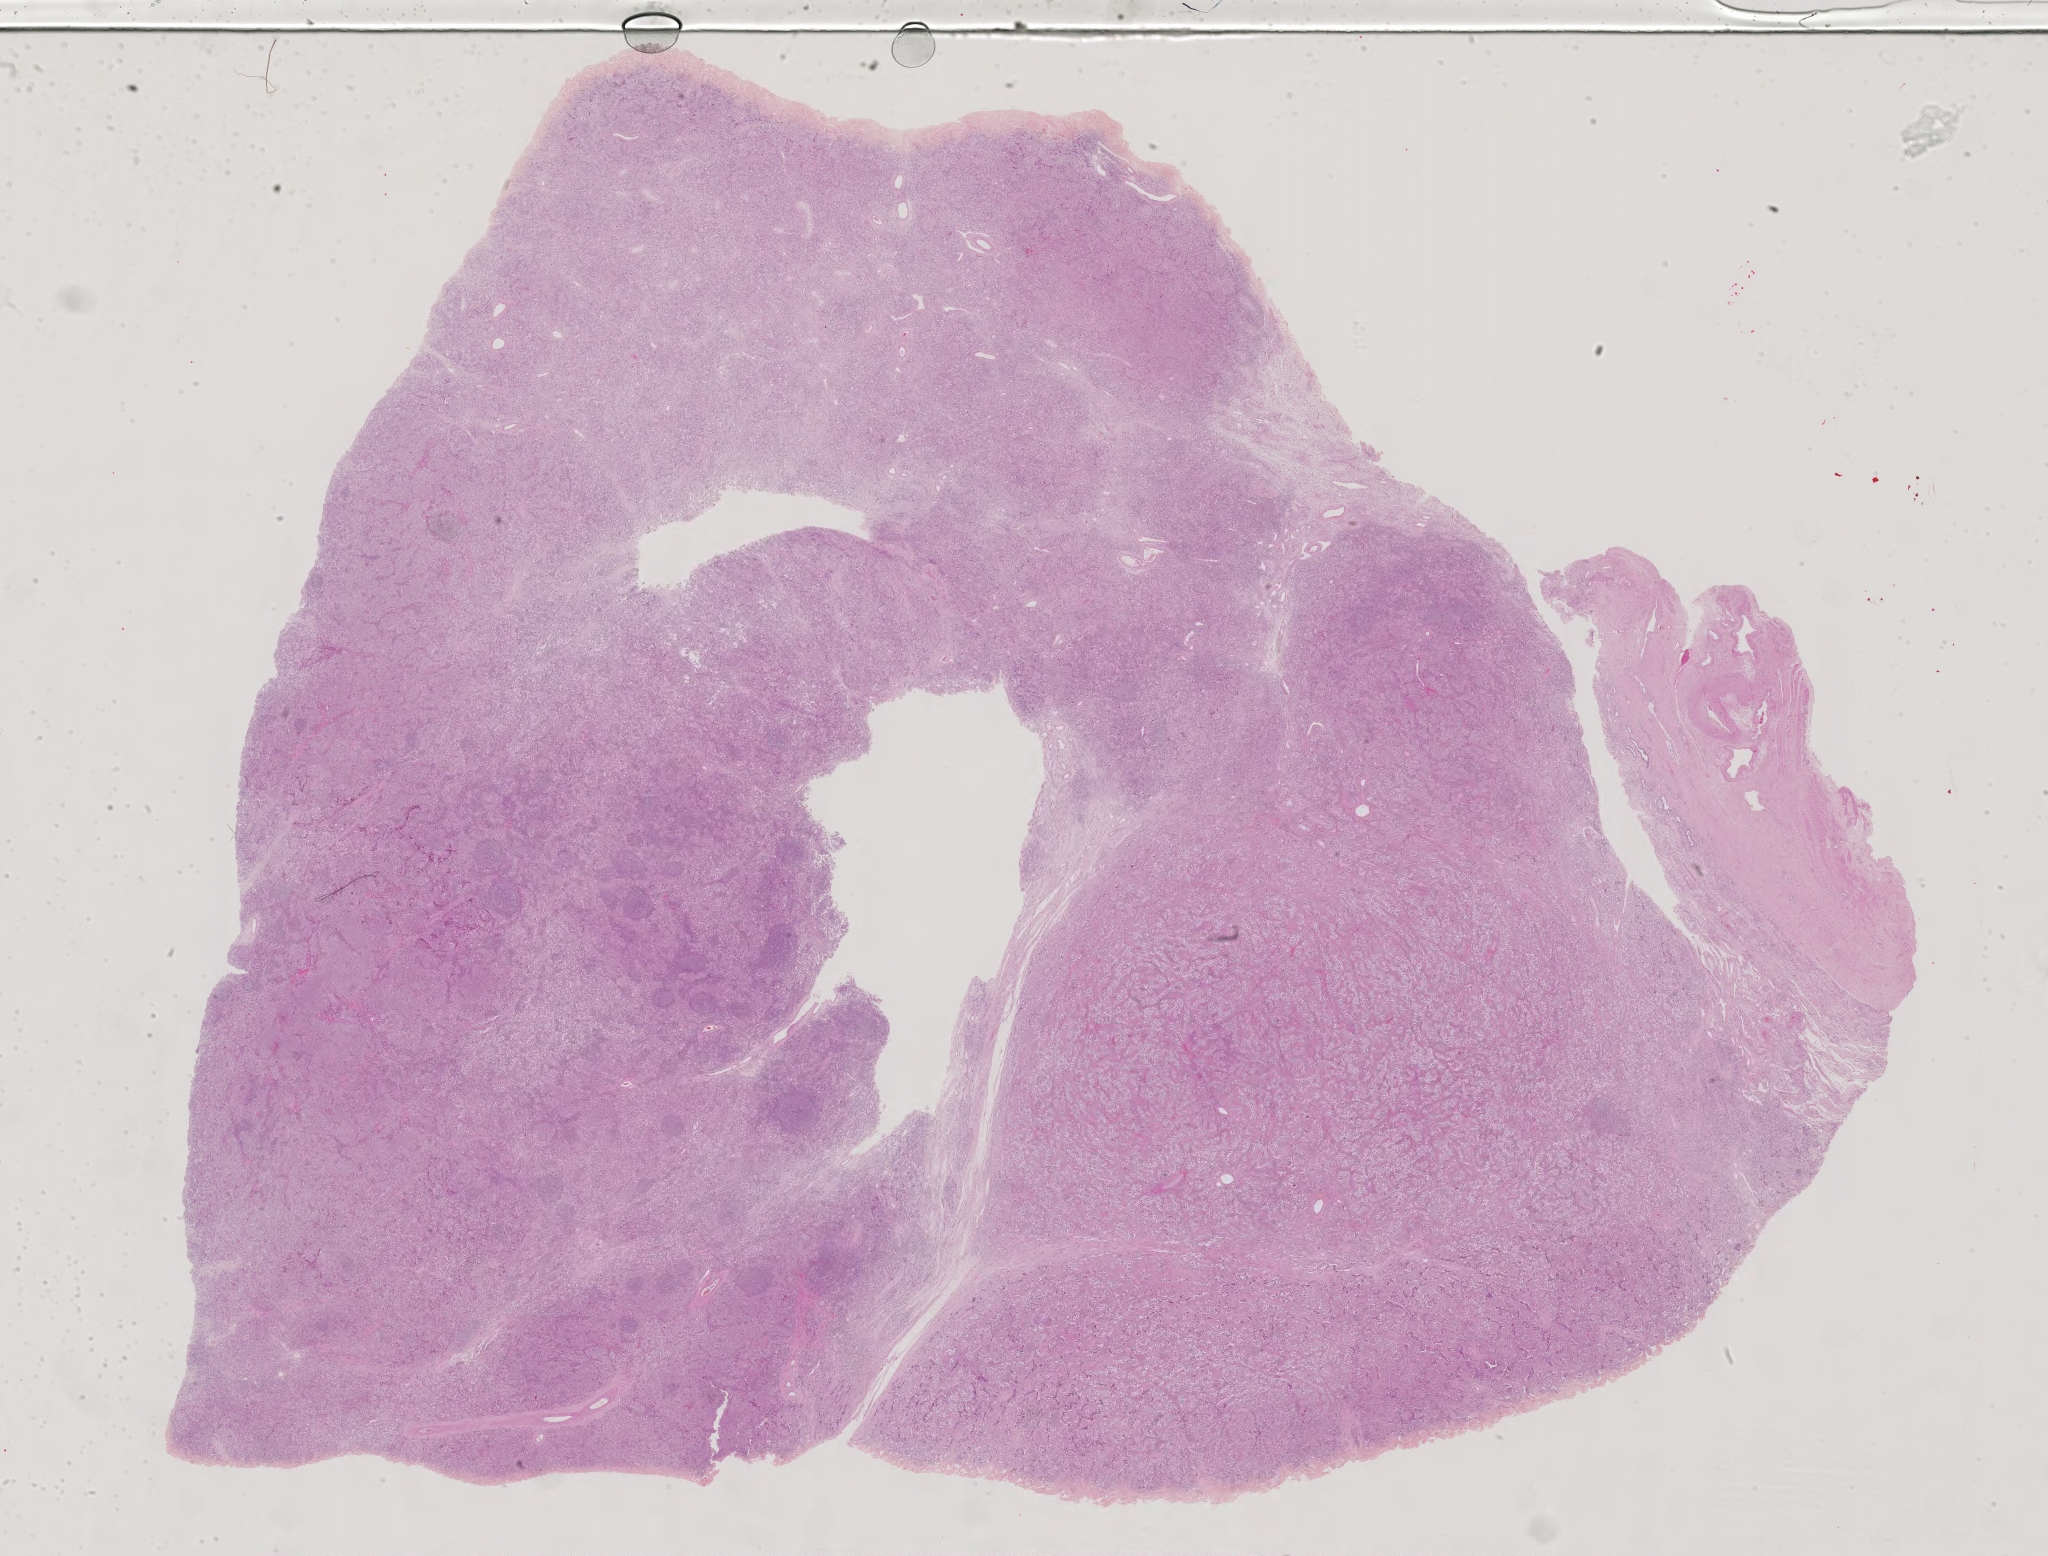
Digitized H&E tissue section (whole slide) — shown as a low-resolution overview of the whole scanned area (about 29.8 x 22.7 mm). FFPE section. Testis, primary tumour sample. Male, age 33 years at initial diagnosis.
- TNM: T1 NX M0
- AJCC pathologic stage: IS (5th edition)
- histologic diagnosis: Seminoma, NOS